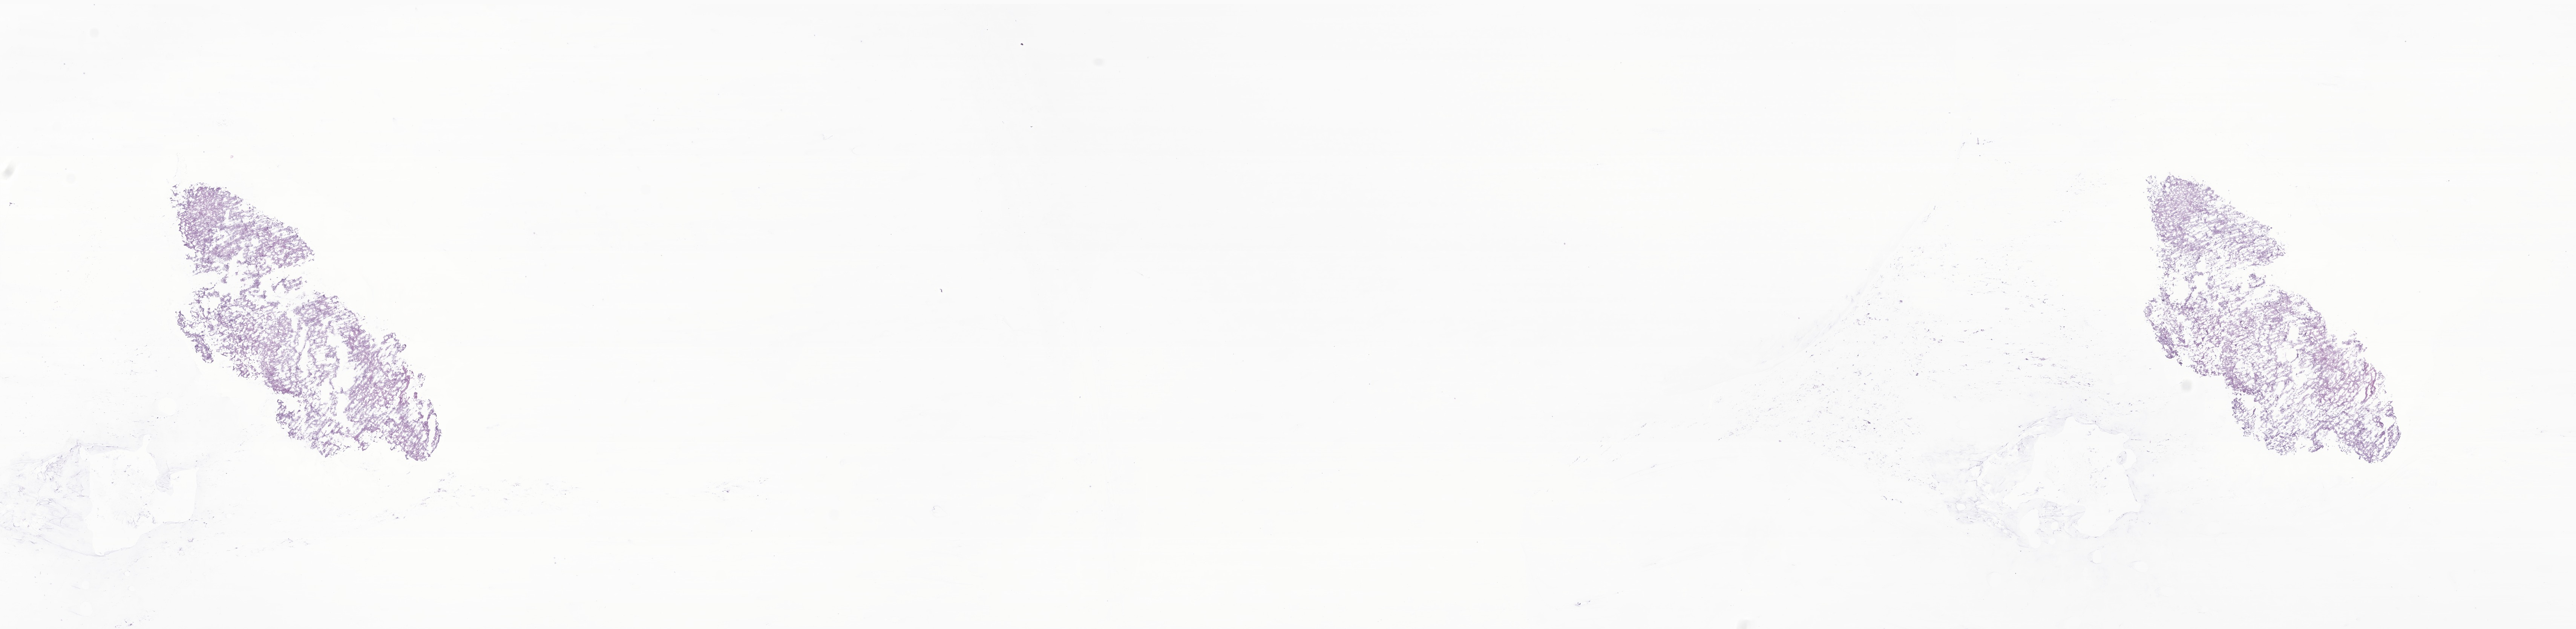
Whole-slide image, hematoxylin and eosin (H&E) stain of tumor tissue from the cerebellum — whole scanned area (about 28.8 x 7.0 mm) shown as a low-resolution overview; frozen section. Patient male; age 69 months (5 years 9 months).
* diagnosis (ICD-O-3 morphology term): Pilocytic astrocytoma